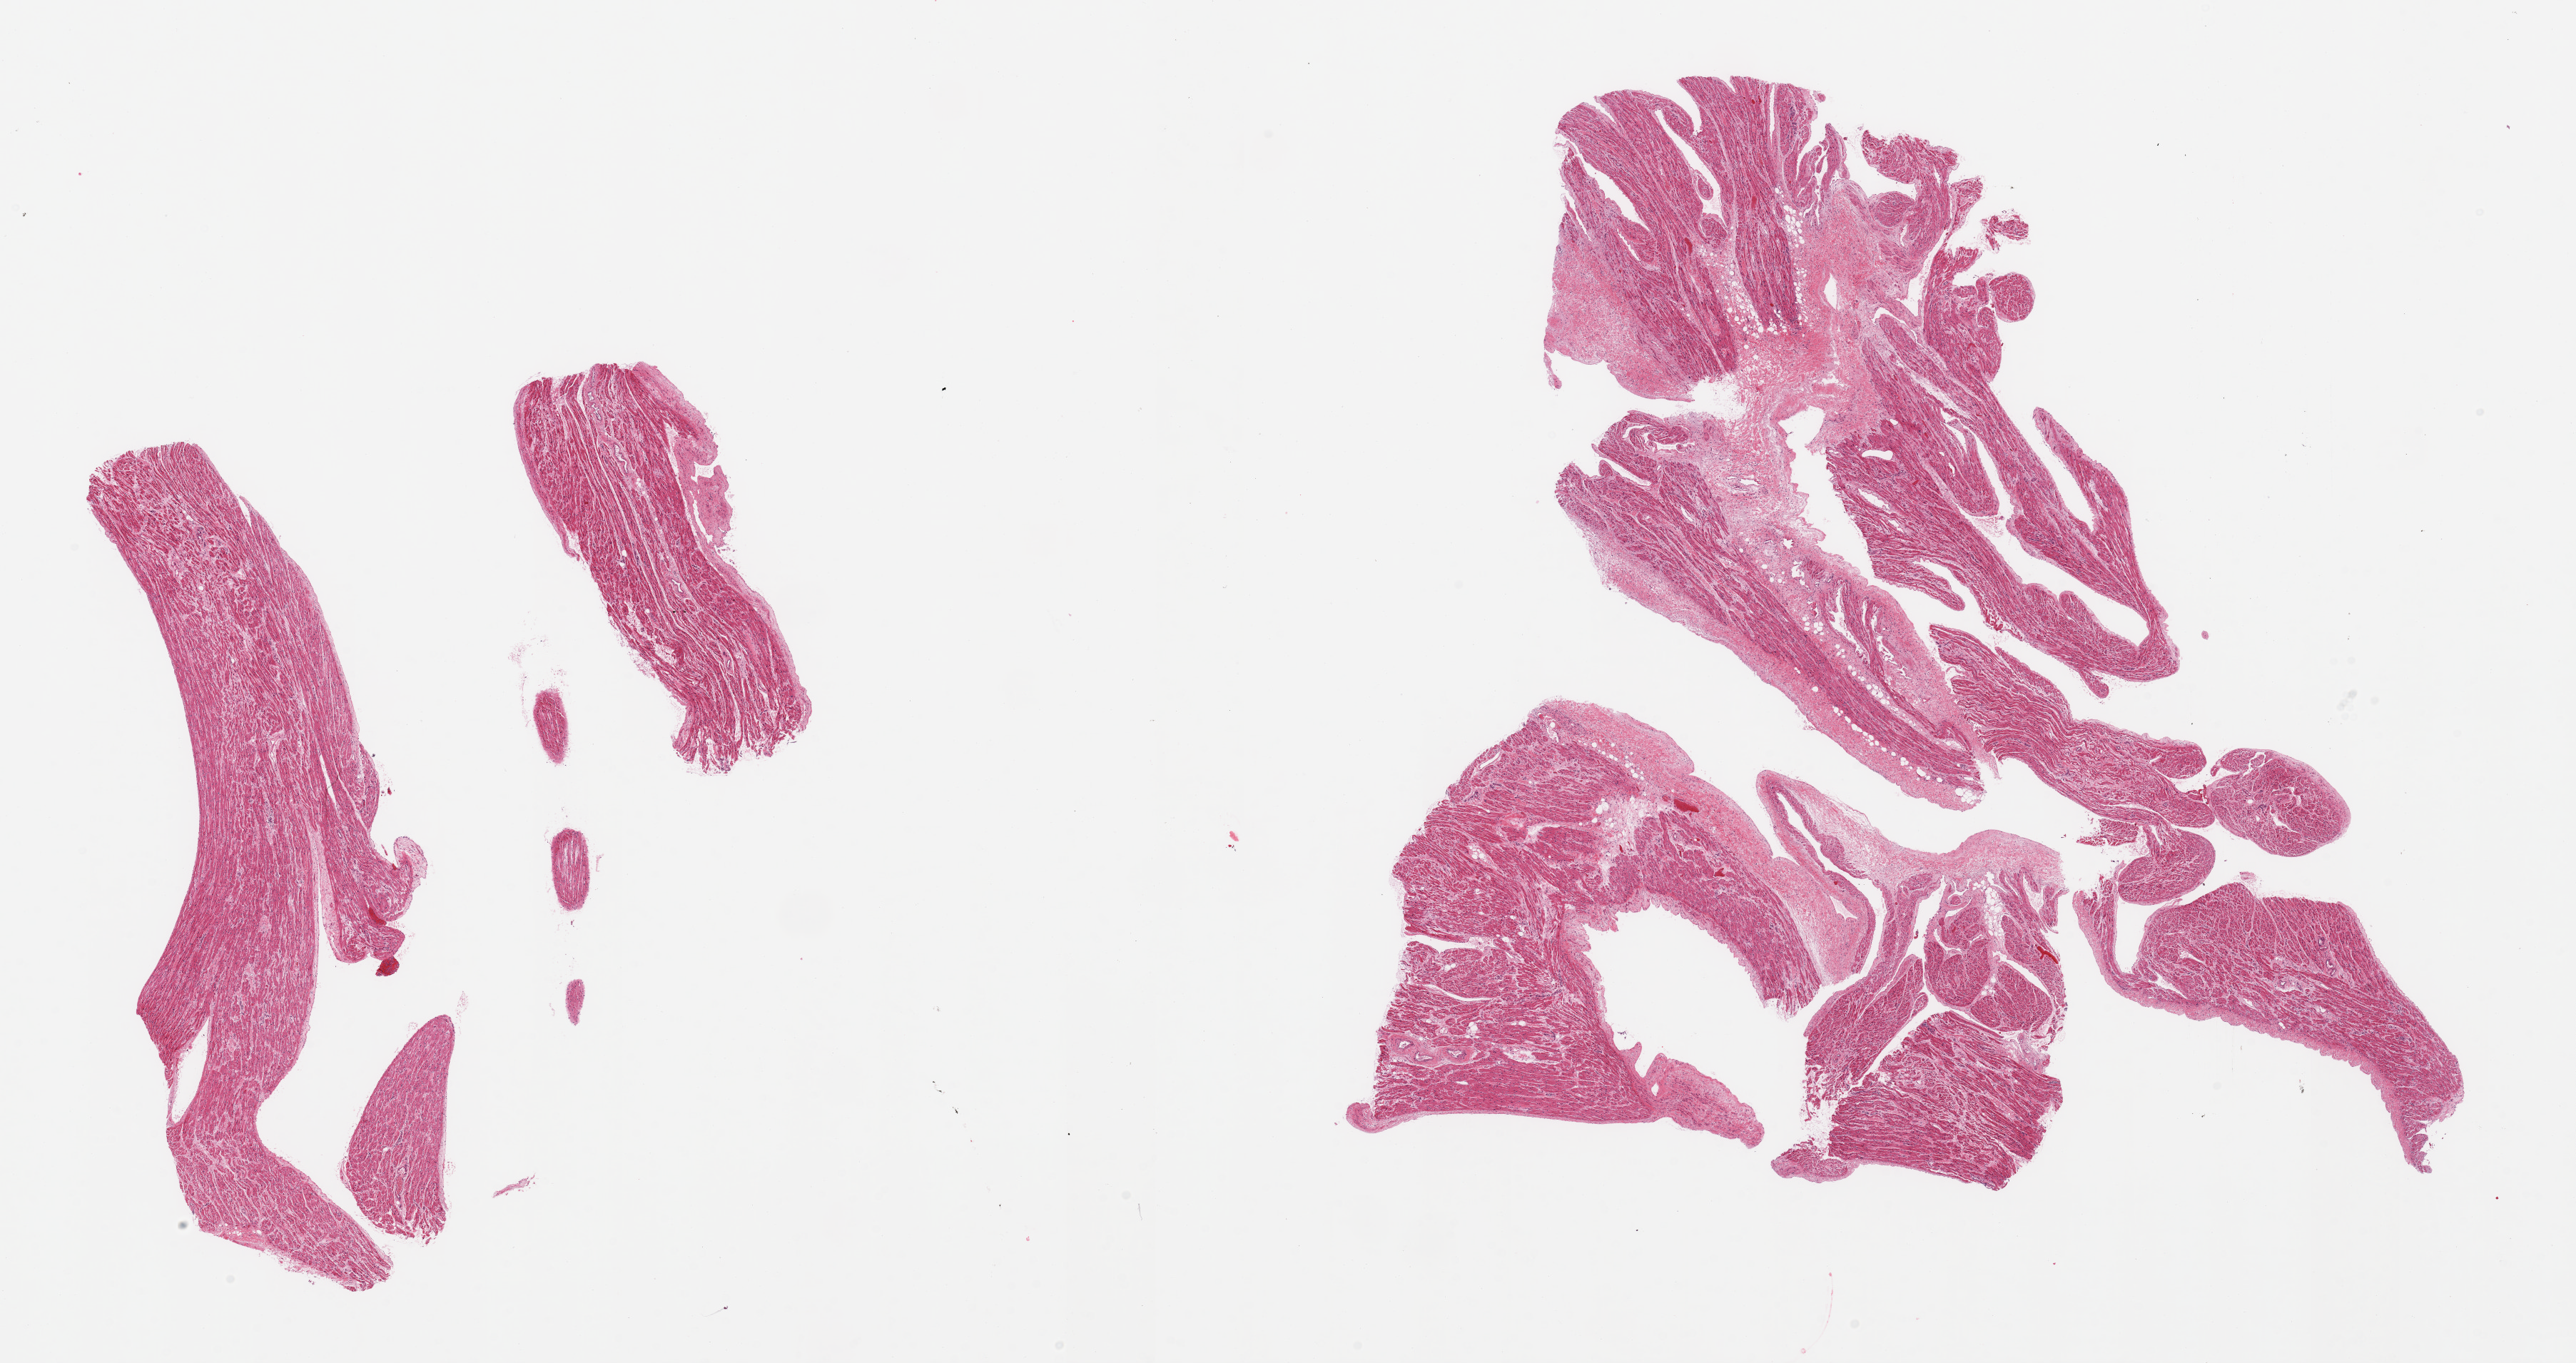
Digitized H&E-stained section, shown as a low-resolution overview of the whole scanned area (about 28.5 x 15.1 mm). PAXgene-fixed paraffin-embedded (PFPE) section. Target tissue: auricular appendage. Donor tissue sample. Male donor.
Reviewer comment on this tissue sample: 2 pieces, fragmented, no abnormalities.